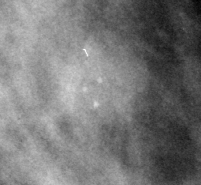
Region of interest cut from a scanned film mammogram (one marked finding); left breast; MLO view.
- Finding: calcifications, morphology punctate / pleomorphic, distribution clustered; BI-RADS assessment category 4; subtlety rating 3 on a 1 (subtle) to 5 (obvious) scale; pathology (as recorded): benign.